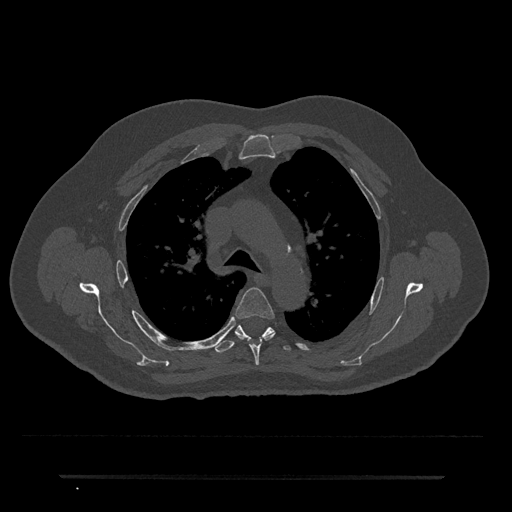
CT including the spine, one axial slice; position 510 of 797 along the scan axis; bone window (W 1800 / L 400 HU); 0.5 mm slice thickness; 512 × 512 image matrix, field of view 437 × 437 mm. Male patient, age 69 years. Case-level facts recorded for this patient, not image findings: primary cancer: prostate.
Structures marked on this image (semi-automatically segmented with operator editing):
- T4 vertebra: box from (x=234, y=287) to (x=275, y=365) px
- T5 vertebra: (x=213, y=324)–(x=291, y=353)